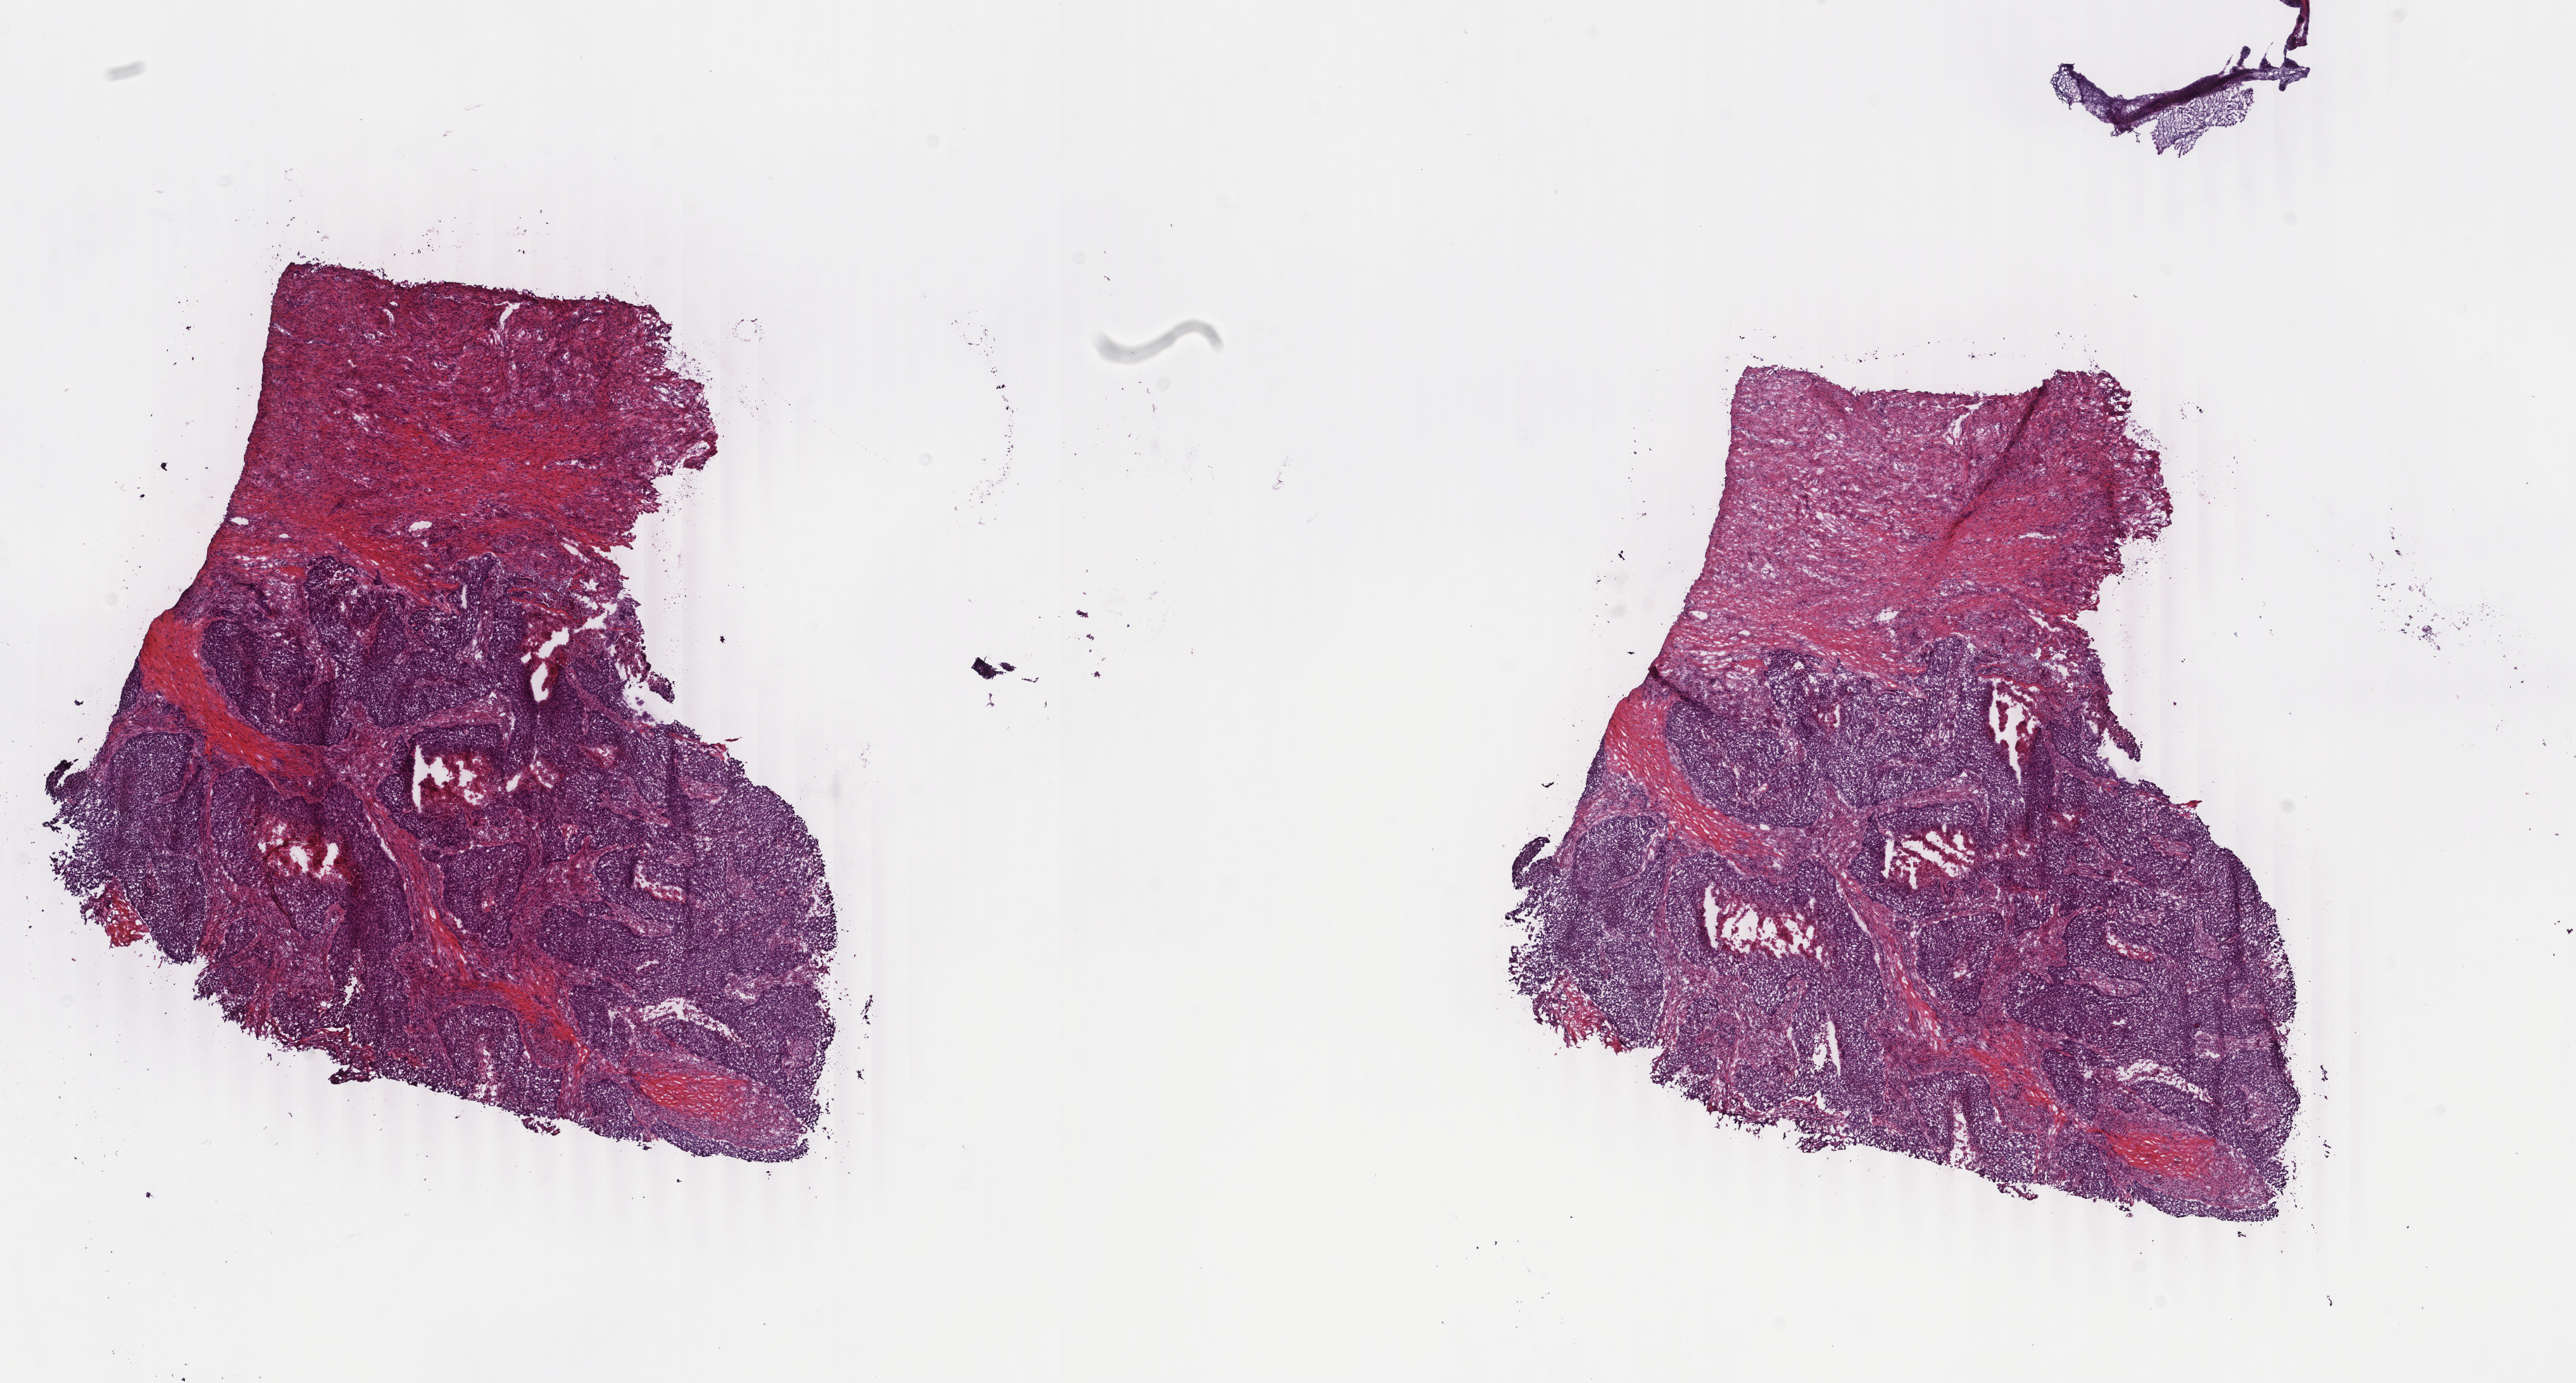
Digitized H&E-stained tissue section (whole slide) — whole scanned area (about 16.2 x 8.7 mm) shown as a low-resolution overview, frozen section from the top of the tissue portion, primary tumour sample from the uterus. Female, age 36 years at initial diagnosis. Histologic grade: G3 (poorly differentiated). Pathologist review of this section (percent, as recorded): tumour cells 70%, tumour nuclei 70%, normal cells 0%, stromal cells 30%, necrosis 0%. Inflammatory infiltration, as recorded: lymphocyte infiltration 40%, monocyte infiltration 20%, neutrophil infiltration 20%.
- lymph nodes positive (case pathology): 0 of 10 examined
- histologic diagnosis: Endometrioid adenocarcinoma, NOS
- FIGO stage: IIIA